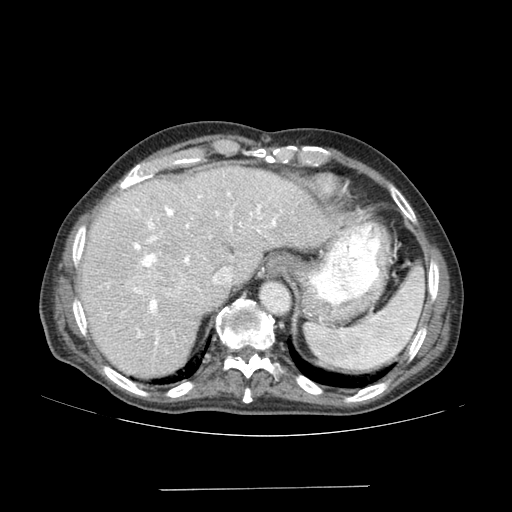
Contrast-enhanced abdominal CT (liver protocol), one axial slice. Slice 124 of 192 in the series (ordered by position). 120 kVp. Soft-tissue window (W 400 / L 40 HU). 2.5 mm slice thickness. 512 × 512 image matrix, field of view 400 × 400 mm. Case-level facts recorded for this patient, not image findings: diagnosis: hepatocellular carcinoma (patient treated with transarterial chemoembolisation; whether this scan precedes or follows treatment is not stated here); TNM stage (as recorded): Stage-IVA; Child-Pugh class: A; tumour differentiation: poorly differentiated; tumour nodularity: uninodular.
Structures marked on this image (semi-automatically segmented with operator editing):
- liver parenchyma outside the tumour (the mass and vessels are separate outlines, so this box may not span the whole liver): bounding box (x1, y1, x2, y2) in pixels: (78, 166, 338, 378)
- mass: (128, 260, 184, 301)
- liver vessels: (133, 192, 277, 344)